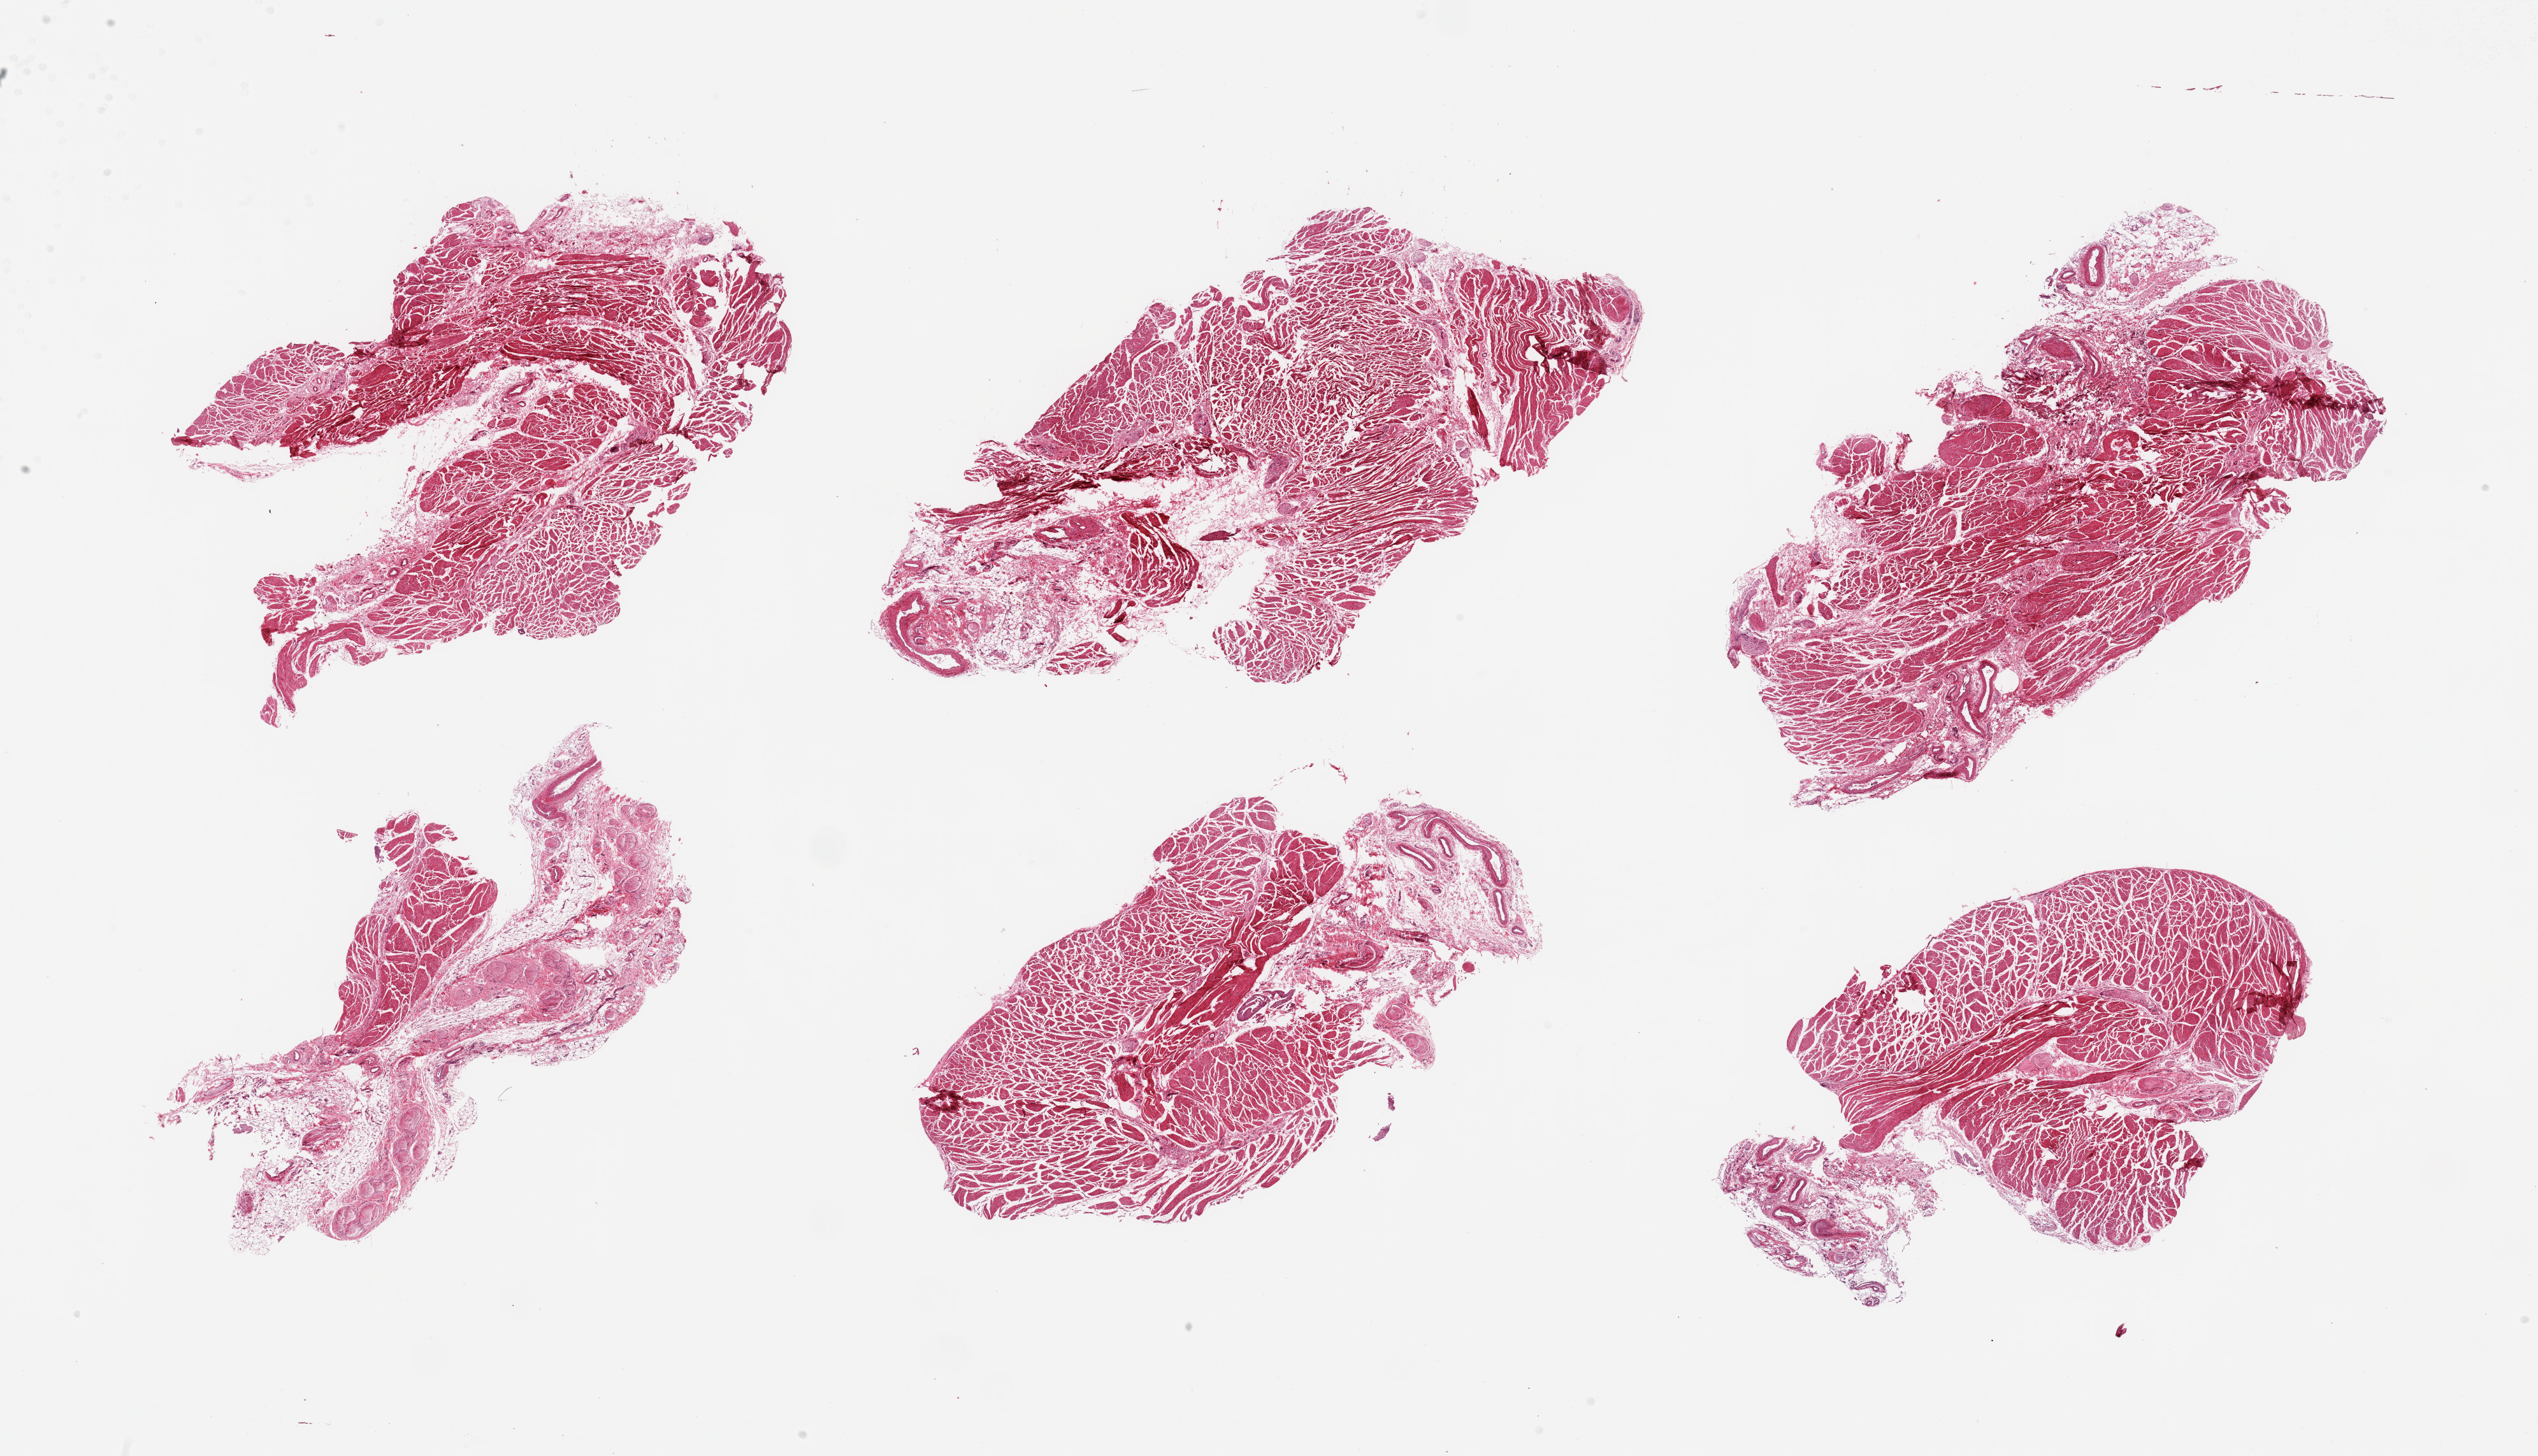
Haematoxylin and eosin whole-slide image, low-resolution overview of the scanned area, about 31.5 x 18.1 mm (acquisition: 20x scan), PAXgene-fixed paraffin-embedded (PFPE) section, target tissue: esophageal muscle, tissue donor sample. Donor sex: male.
- review note (as recorded): 6 pieces; 1 piece contains 70% adventitial nerves; another piece contains focus of mucosal carry-over